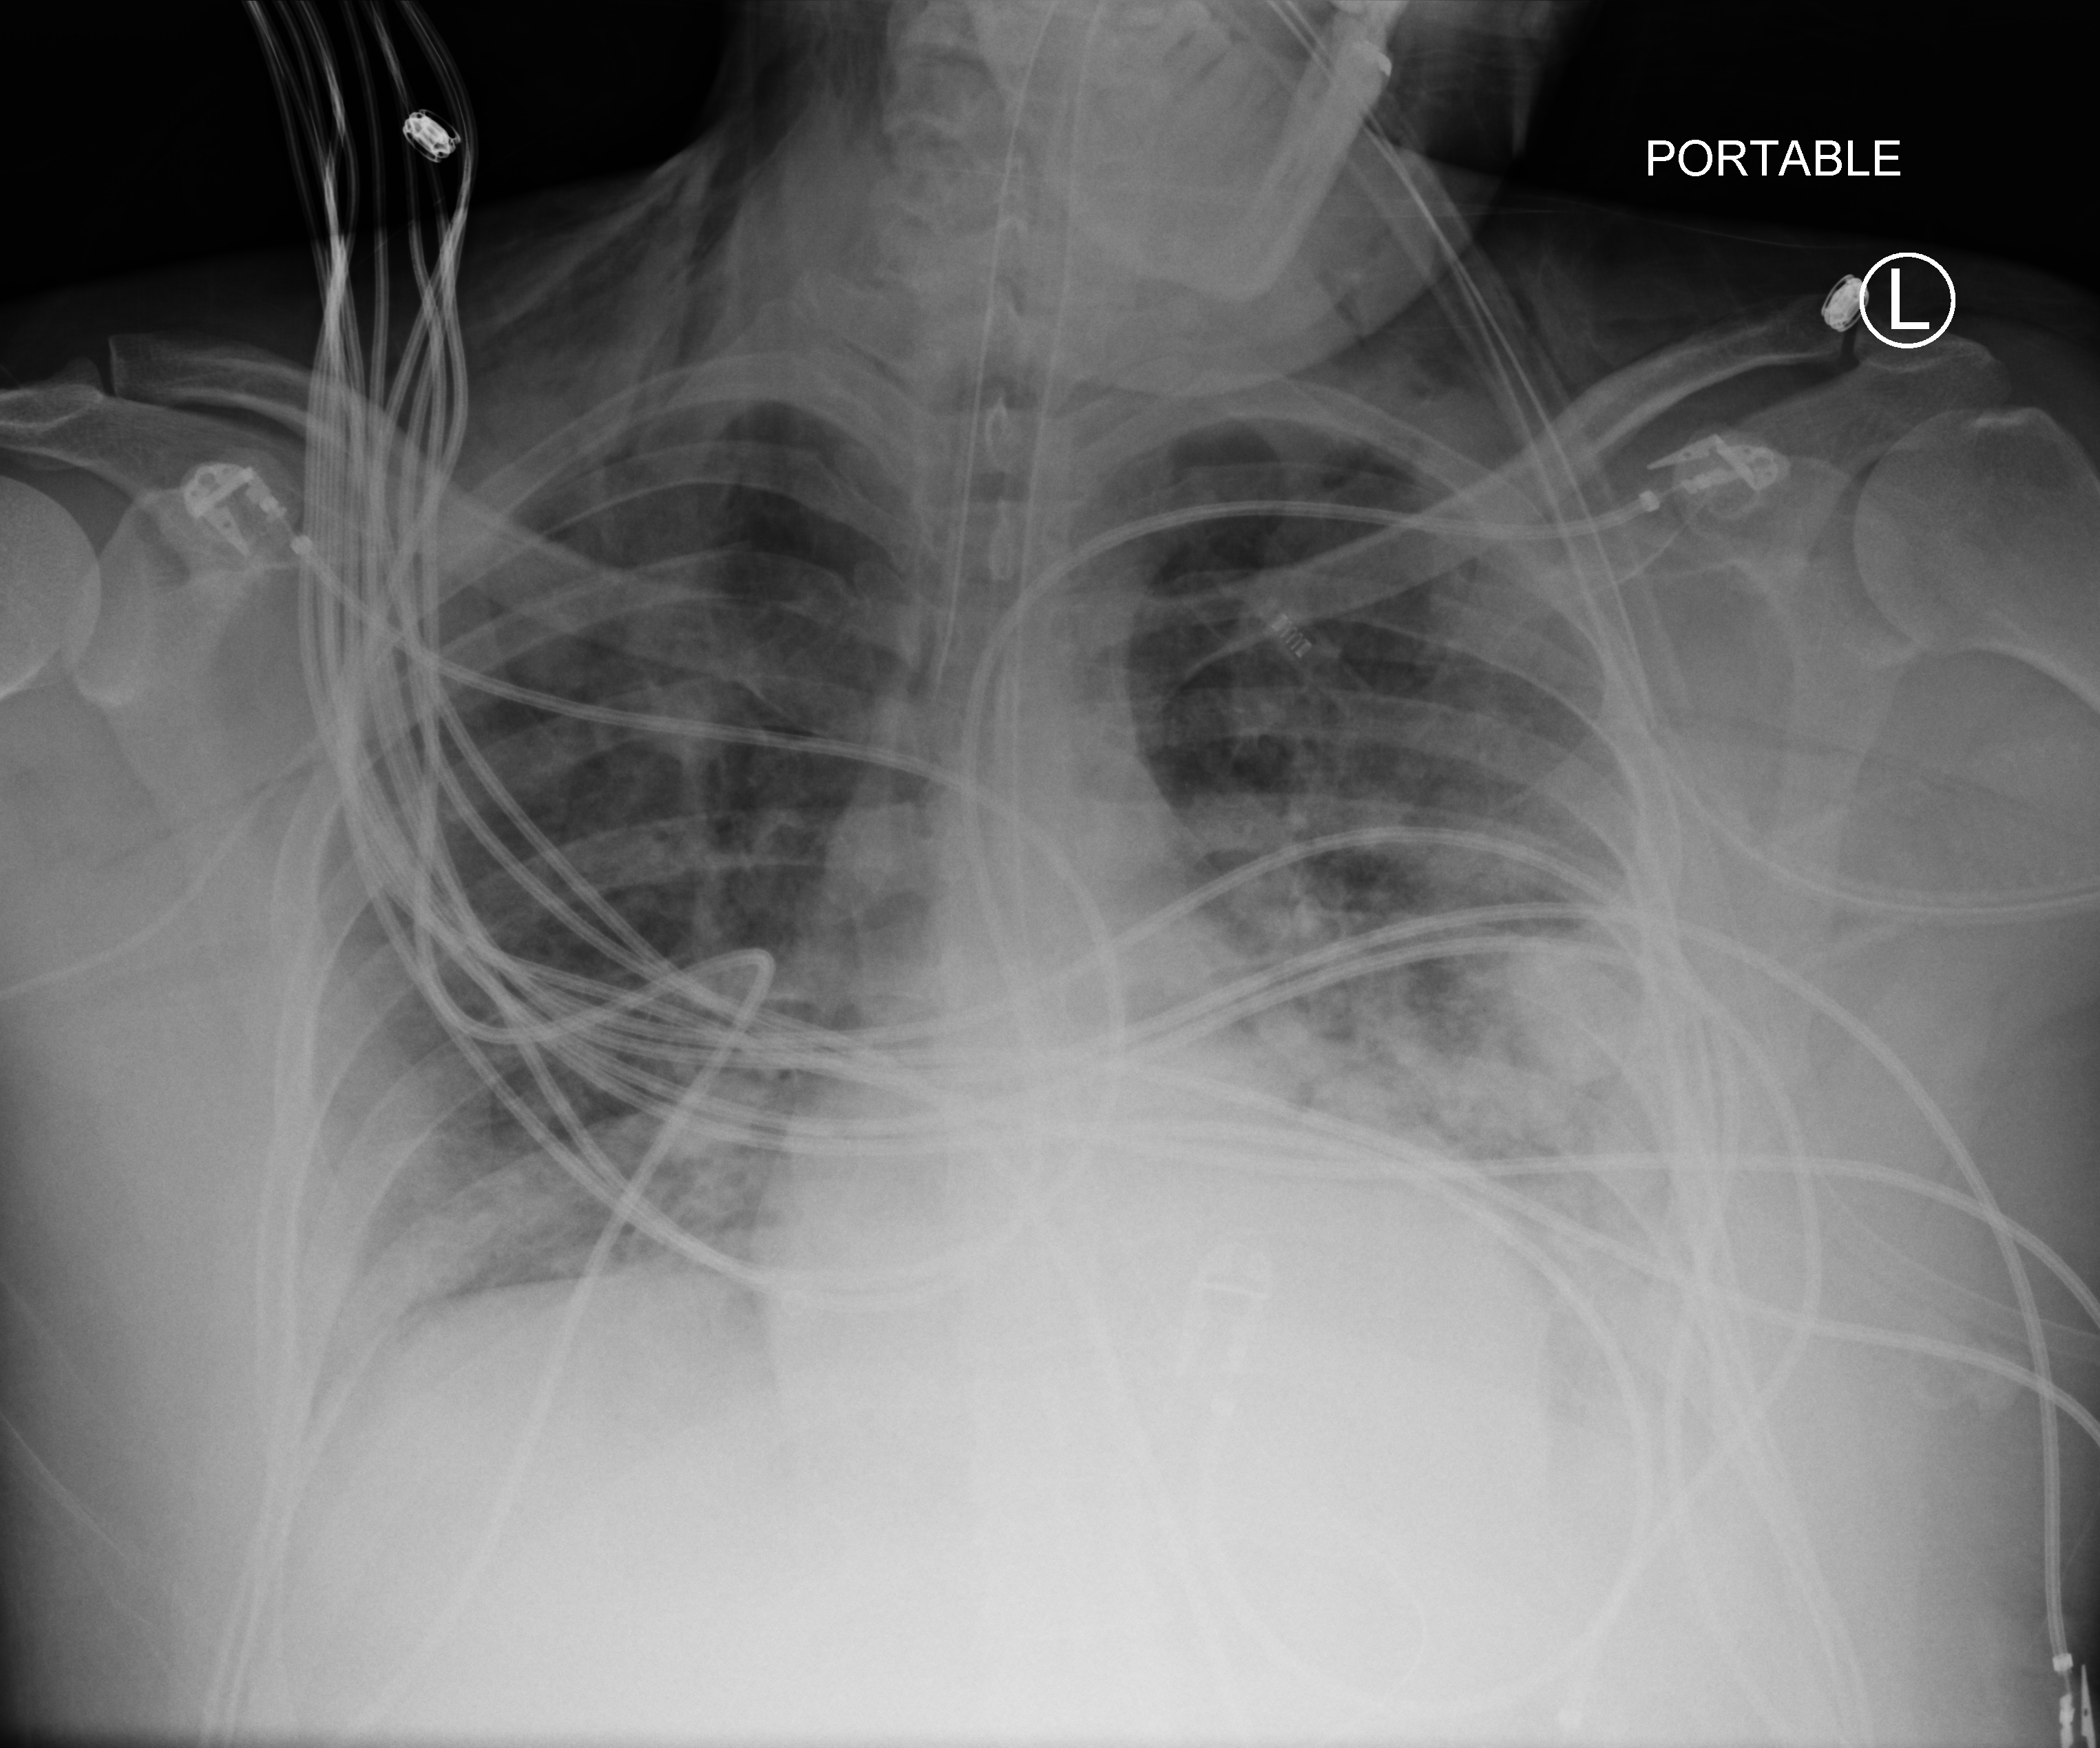
Portable chest radiograph; anteroposterior (AP) projection. Patient hospitalised with COVID-19; male, aged 18–59 years.
Hospital-stay facts (about this admission, not read from this image; timing relative to this image not recorded): mechanically ventilated during this hospital stay: yes; diabetes (admission record): no; admitted to intensive care during this hospital stay: yes.